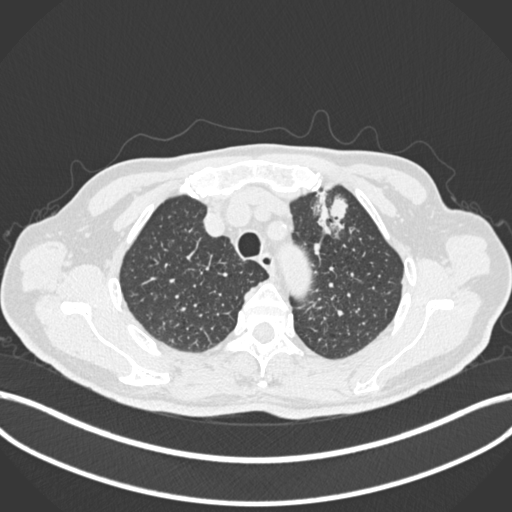
Chest CT, one axial slice; position 208 of 261 along the scan axis; reconstruction kernel B30f; lung window (W 1500 / L -600 HU); 512 × 512 image matrix, field of view 400 × 400 mm. Patient: male, 74 years. From the clinical record (not read from this slice): clinical TNM (as recorded): T2b N0 M1c.
Structures marked on this image (rectangle marked by the reading radiologist):
- lung tumour (recorded histology: adenocarcinoma): bounding box [x1, y1, x2, y2] px = [312, 190, 353, 239]